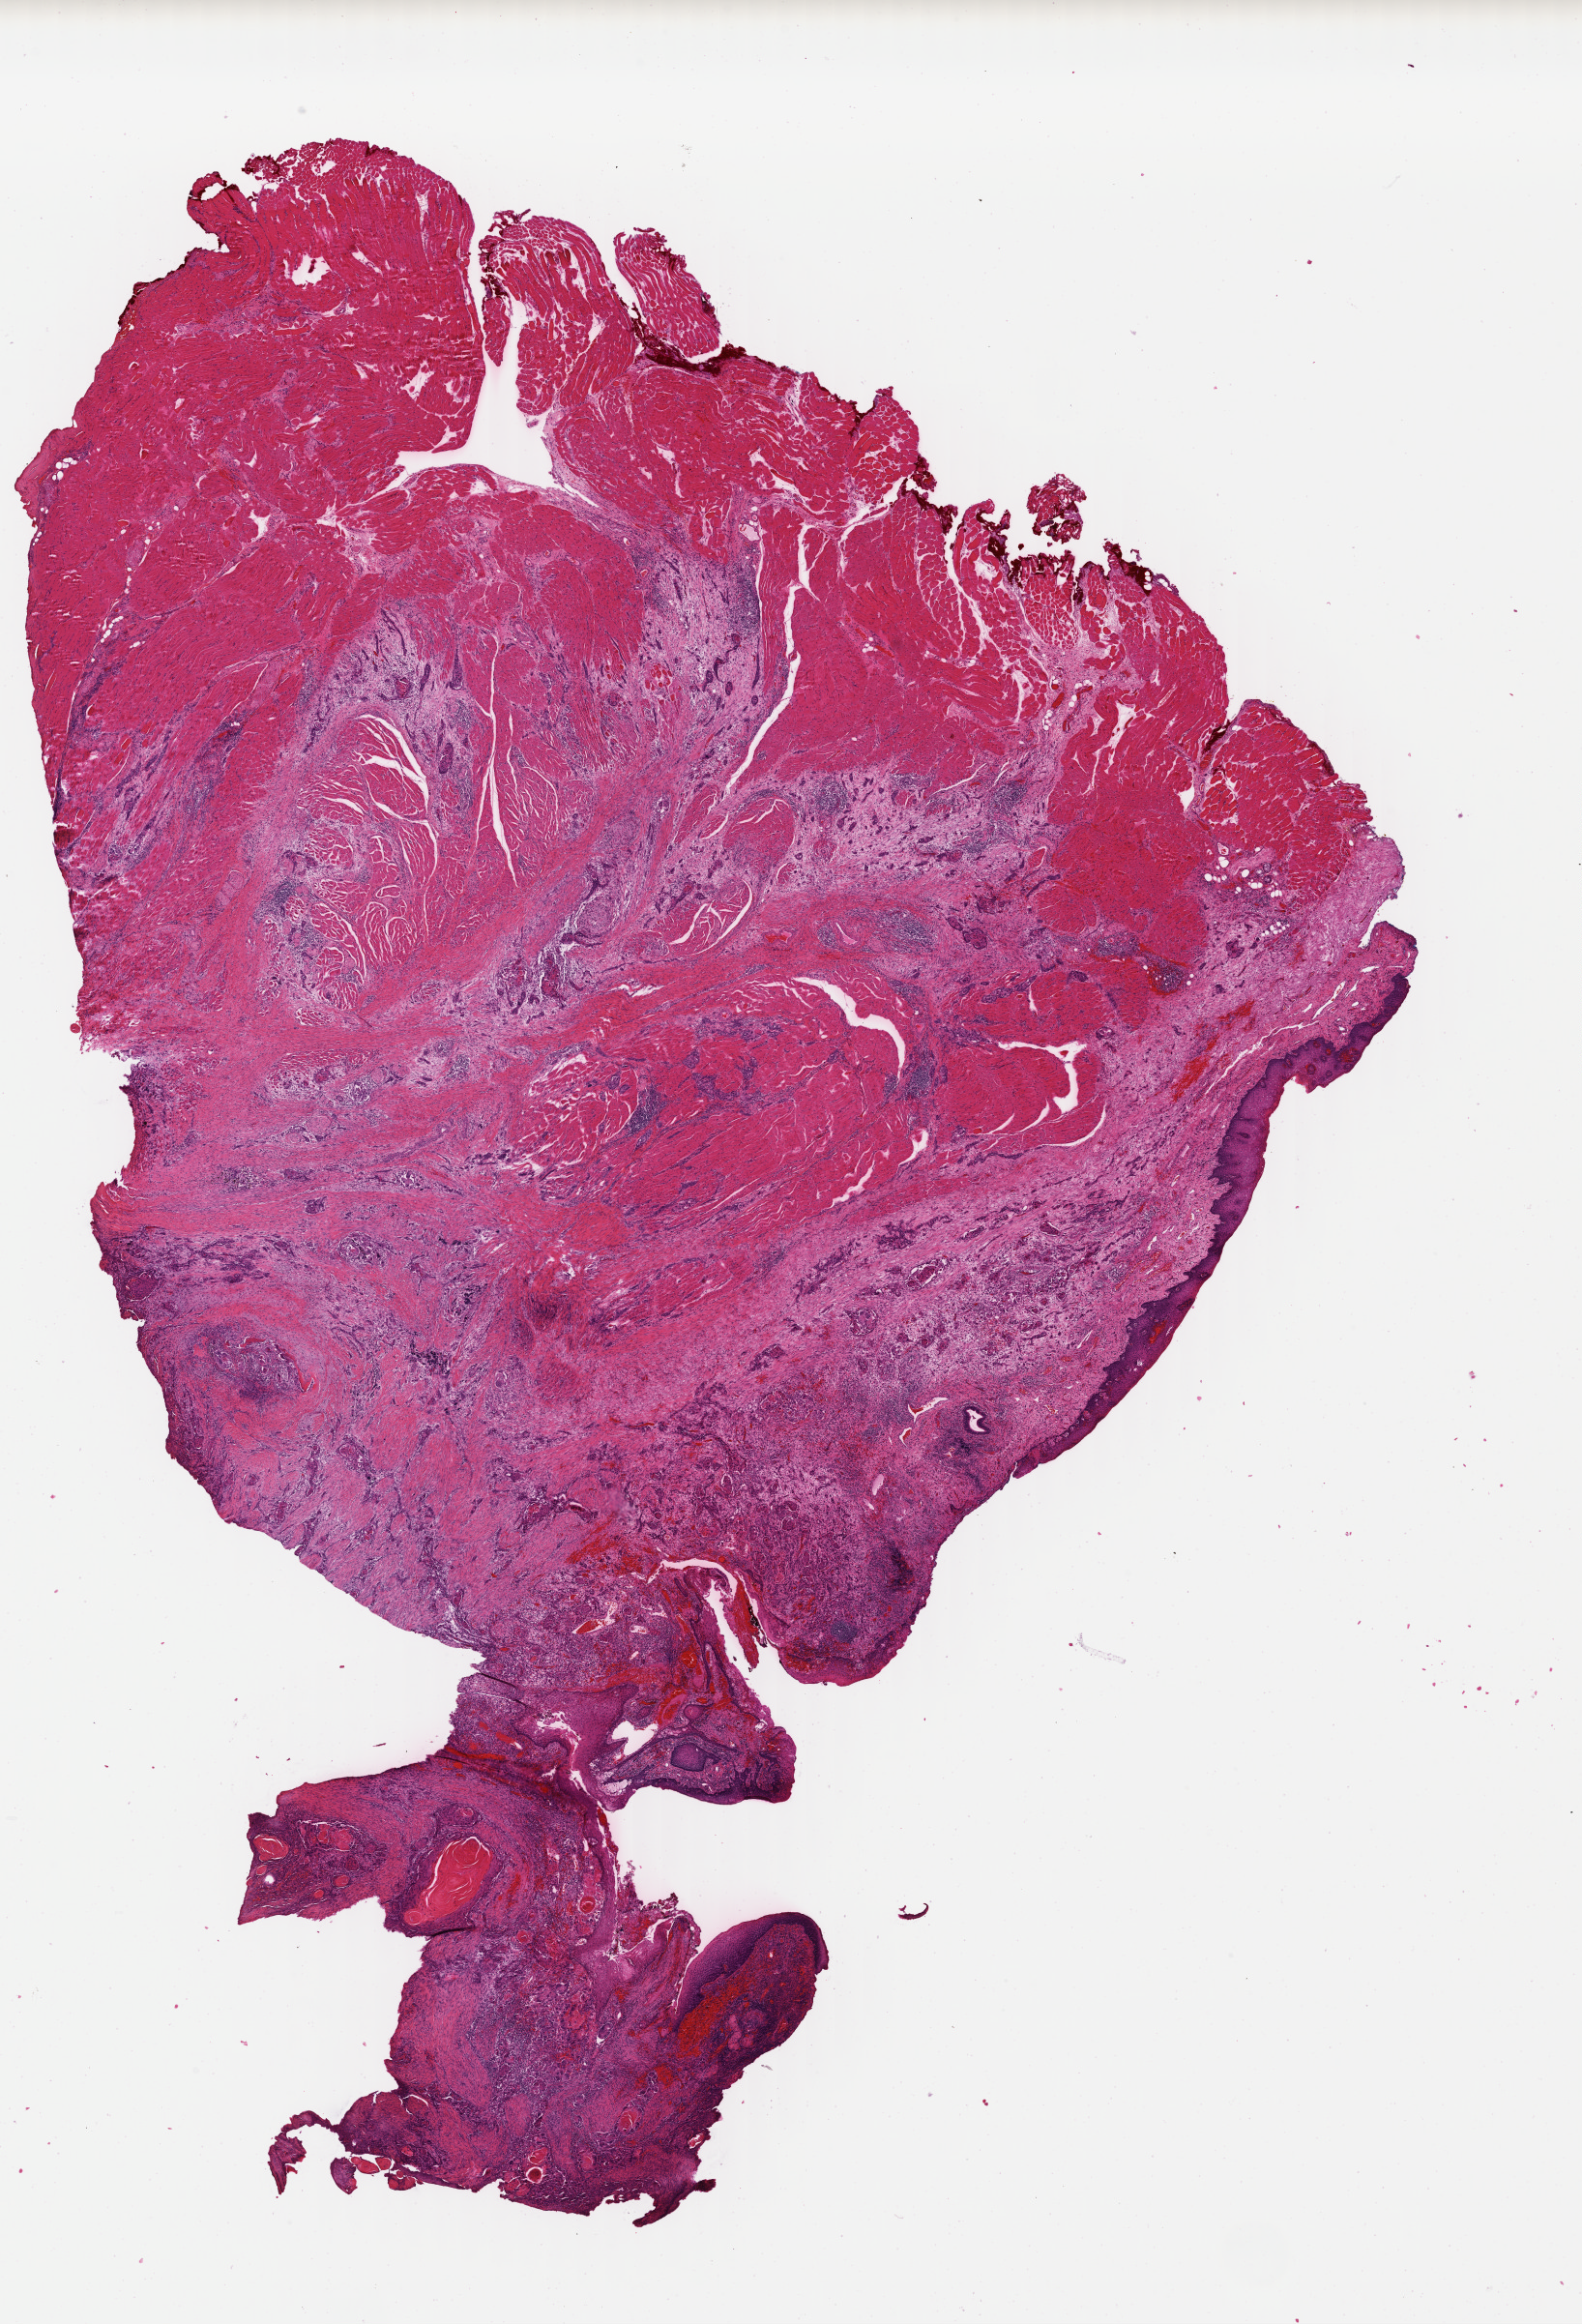
Hematoxylin and eosin (H&E) stained whole-slide image, a low-resolution overview of the entire scanned area, about 12.9 x 18.9 mm (acquisition: 40x scan), formalin-fixed paraffin-embedded (FFPE) diagnostic section, sample: primary tumour, head and neck. Patient: female, age at initial diagnosis 69 years. Histologic grade: G3 (poorly differentiated).
AJCC pathologic stage: IVA (6th edition). Pathologic diagnosis: Squamous cell carcinoma, NOS (hypopharynx, NOS).